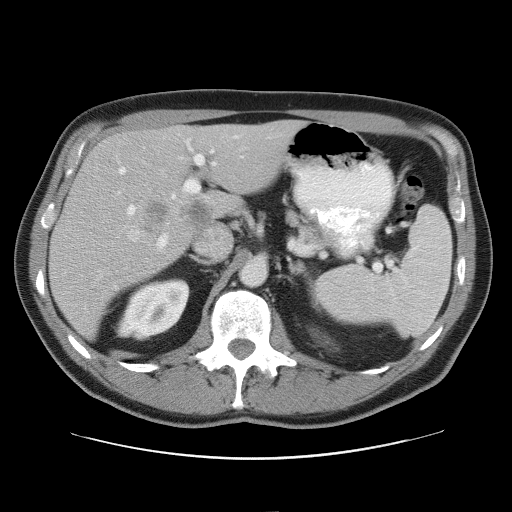
Contrast-enhanced abdominal CT, one axial slice. Position 36 of 52 along the scan axis. 120 kVp. Intravenous contrast given. Soft-tissue window (W 400 / L 40 HU). 512 × 512 image matrix, field of view 393 × 393 mm. Male patient, age 70 years. Case-level facts recorded for this patient, not image findings: diagnosis: colorectal cancer liver metastases, imaged before liver resection; multiple liver metastases: yes; largest metastasis: 4 cm.
Structures marked on this image (outlined manually by an expert reader):
- hepatic veins: bounding box [x1, y1, x2, y2] px = [128, 147, 246, 242]
- liver: [49, 121, 301, 339]
- planned liver remnant (the part of the liver to remain after resection): [106, 122, 302, 196]
- portal vein (with intrahepatic branches): [118, 136, 272, 250]
- liver metastasis: [182, 202, 213, 226]
- liver metastasis: [146, 204, 171, 233]